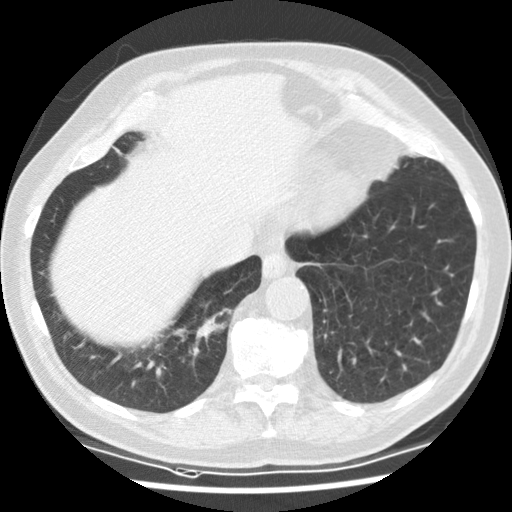
Low-dose screening chest CT, one axial slice. 120 kVp. Lung window (W 1500 / L -600 HU). 2.5 mm slice thickness. 512 × 512 image matrix, field of view 340 × 340 mm.
Outlined on this slice (expert manual segmentation):
- lesion 2 (nodule, upper lobe of right lung): box from (x=195, y=308) to (x=232, y=350) px